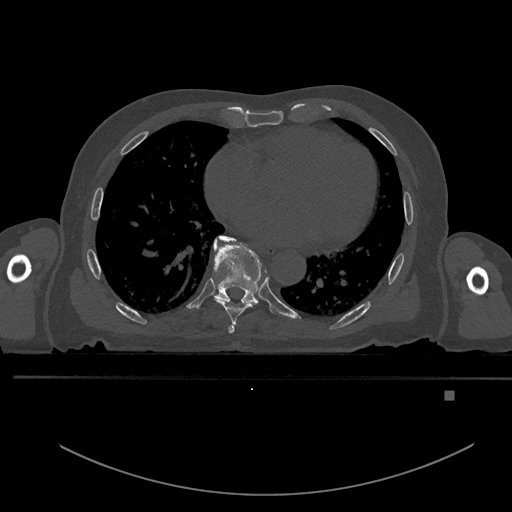
CT including the spine, one axial slice. Slice 228 of 969 in the series (ordered by position). Bone window (W 1800 / L 400 HU). 0.5 mm slice thickness. 512 × 512 image matrix, field of view 456 × 456 mm. Male patient, age 82 years. From the clinical record (not read from this slice): primary cancer: prostate; vertebrae with lytic lesions (as recorded): T11, T9, T8, T2.
Outlined on this slice (semi-automatically segmented with operator editing):
- T6 vertebra: box from (x=228, y=325) to (x=234, y=333) px
- T7 vertebra: (x=217, y=235)–(x=267, y=325)
- T8 vertebra: (x=213, y=237)–(x=262, y=308)